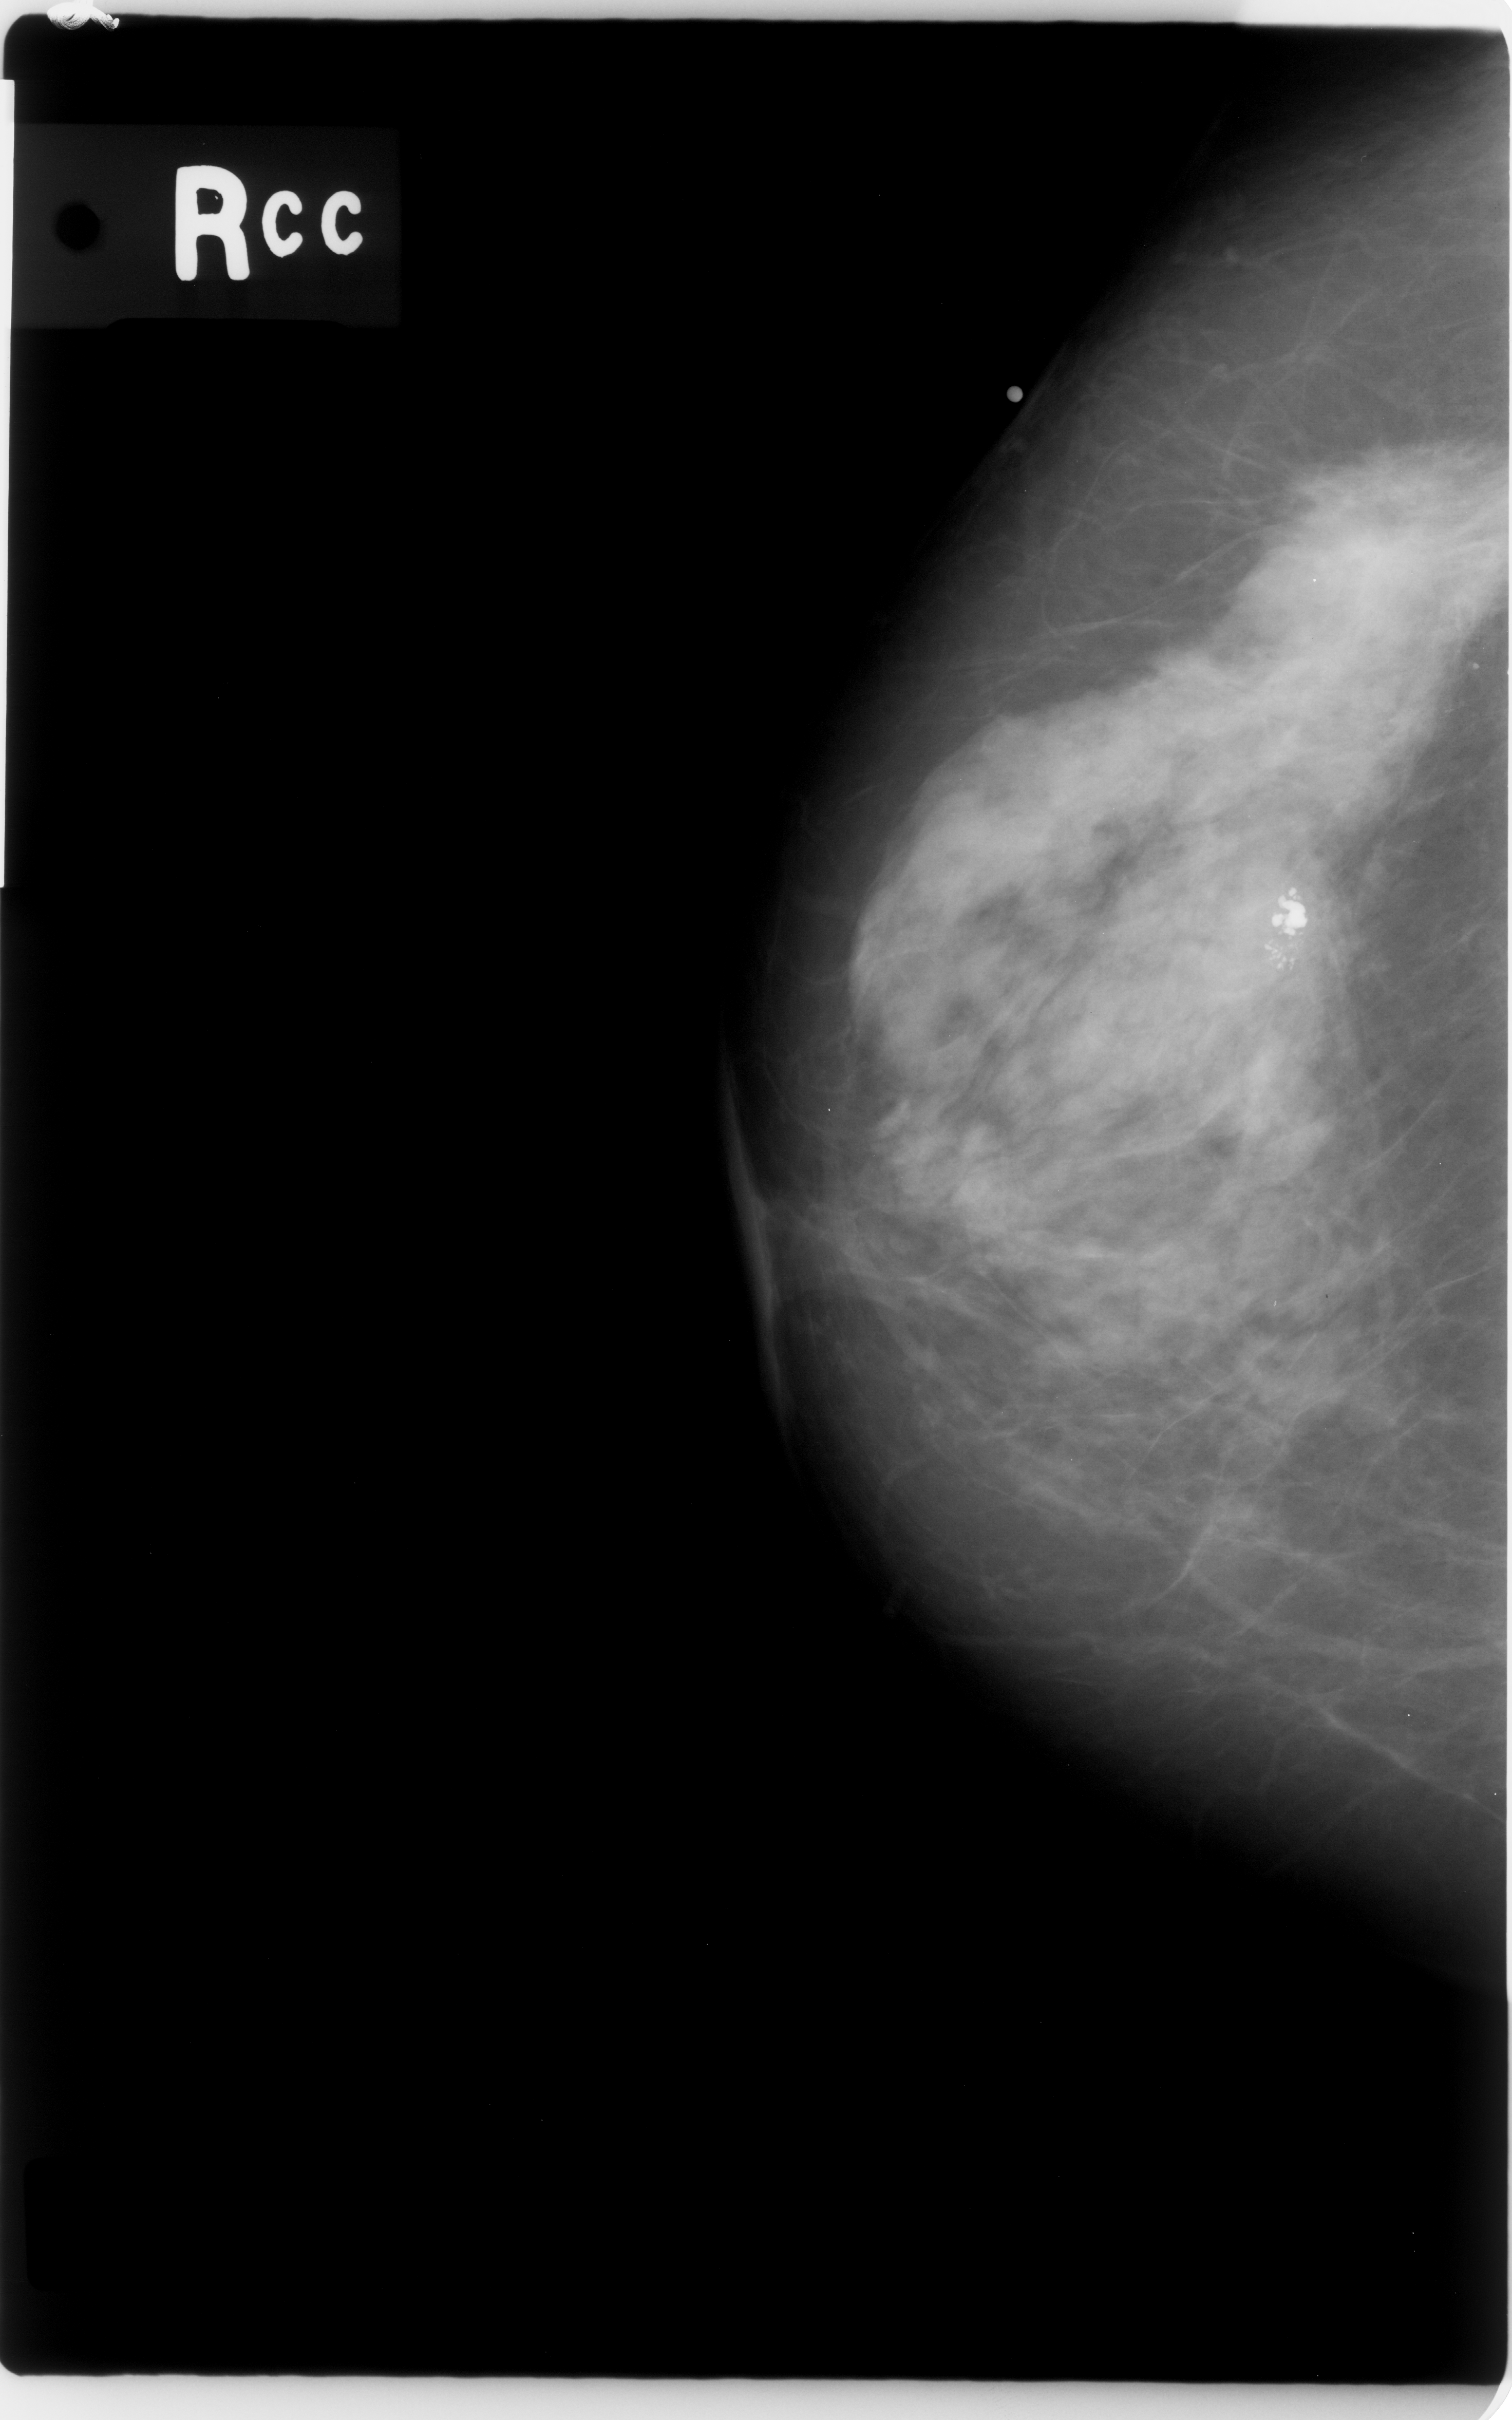
Mammogram (digitized film). Right breast. Craniocaudal (CC) view. Breast composition: heterogeneously dense (BI-RADS density category 3 of 4). 1512 × 2420 image matrix.
Marked abnormalities (boxes around the expert regions of interest):
- mass, shape irregular, margins spiculated; BI-RADS assessment category 5; pathology result (as recorded, not read from the image): malignant: bounding box [x1, y1, x2, y2] px = [1248, 460, 1440, 653]